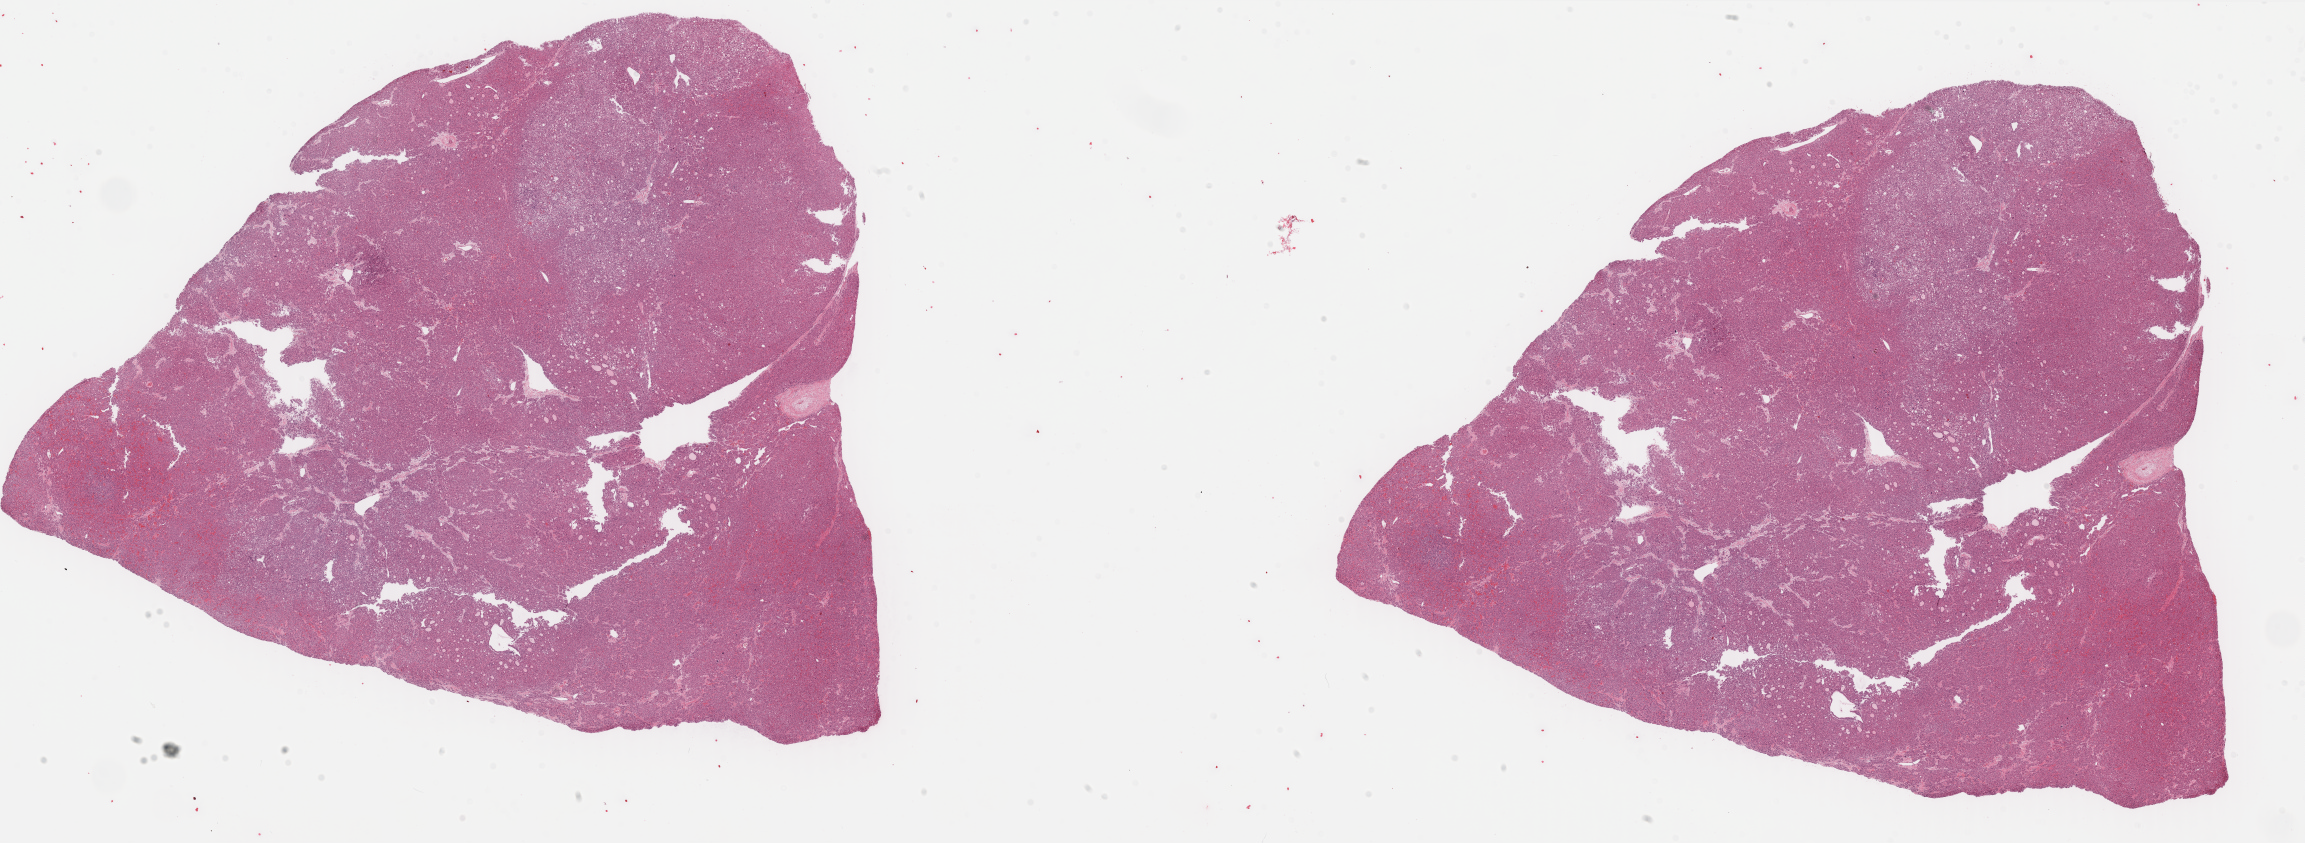
H&E whole-slide image, low-resolution overview of the scanned area, about 36.5 x 13.3 mm (slide scanned at 40x). FFPE section. Primary tumour sample from the liver. Female patient; age at initial diagnosis 66 years. Histologic grade: G2 (moderately differentiated).
• AJCC pathologic stage: I (7th edition)
• histologic diagnosis: Hepatocellular carcinoma, NOS
• TNM: T1 NX M0